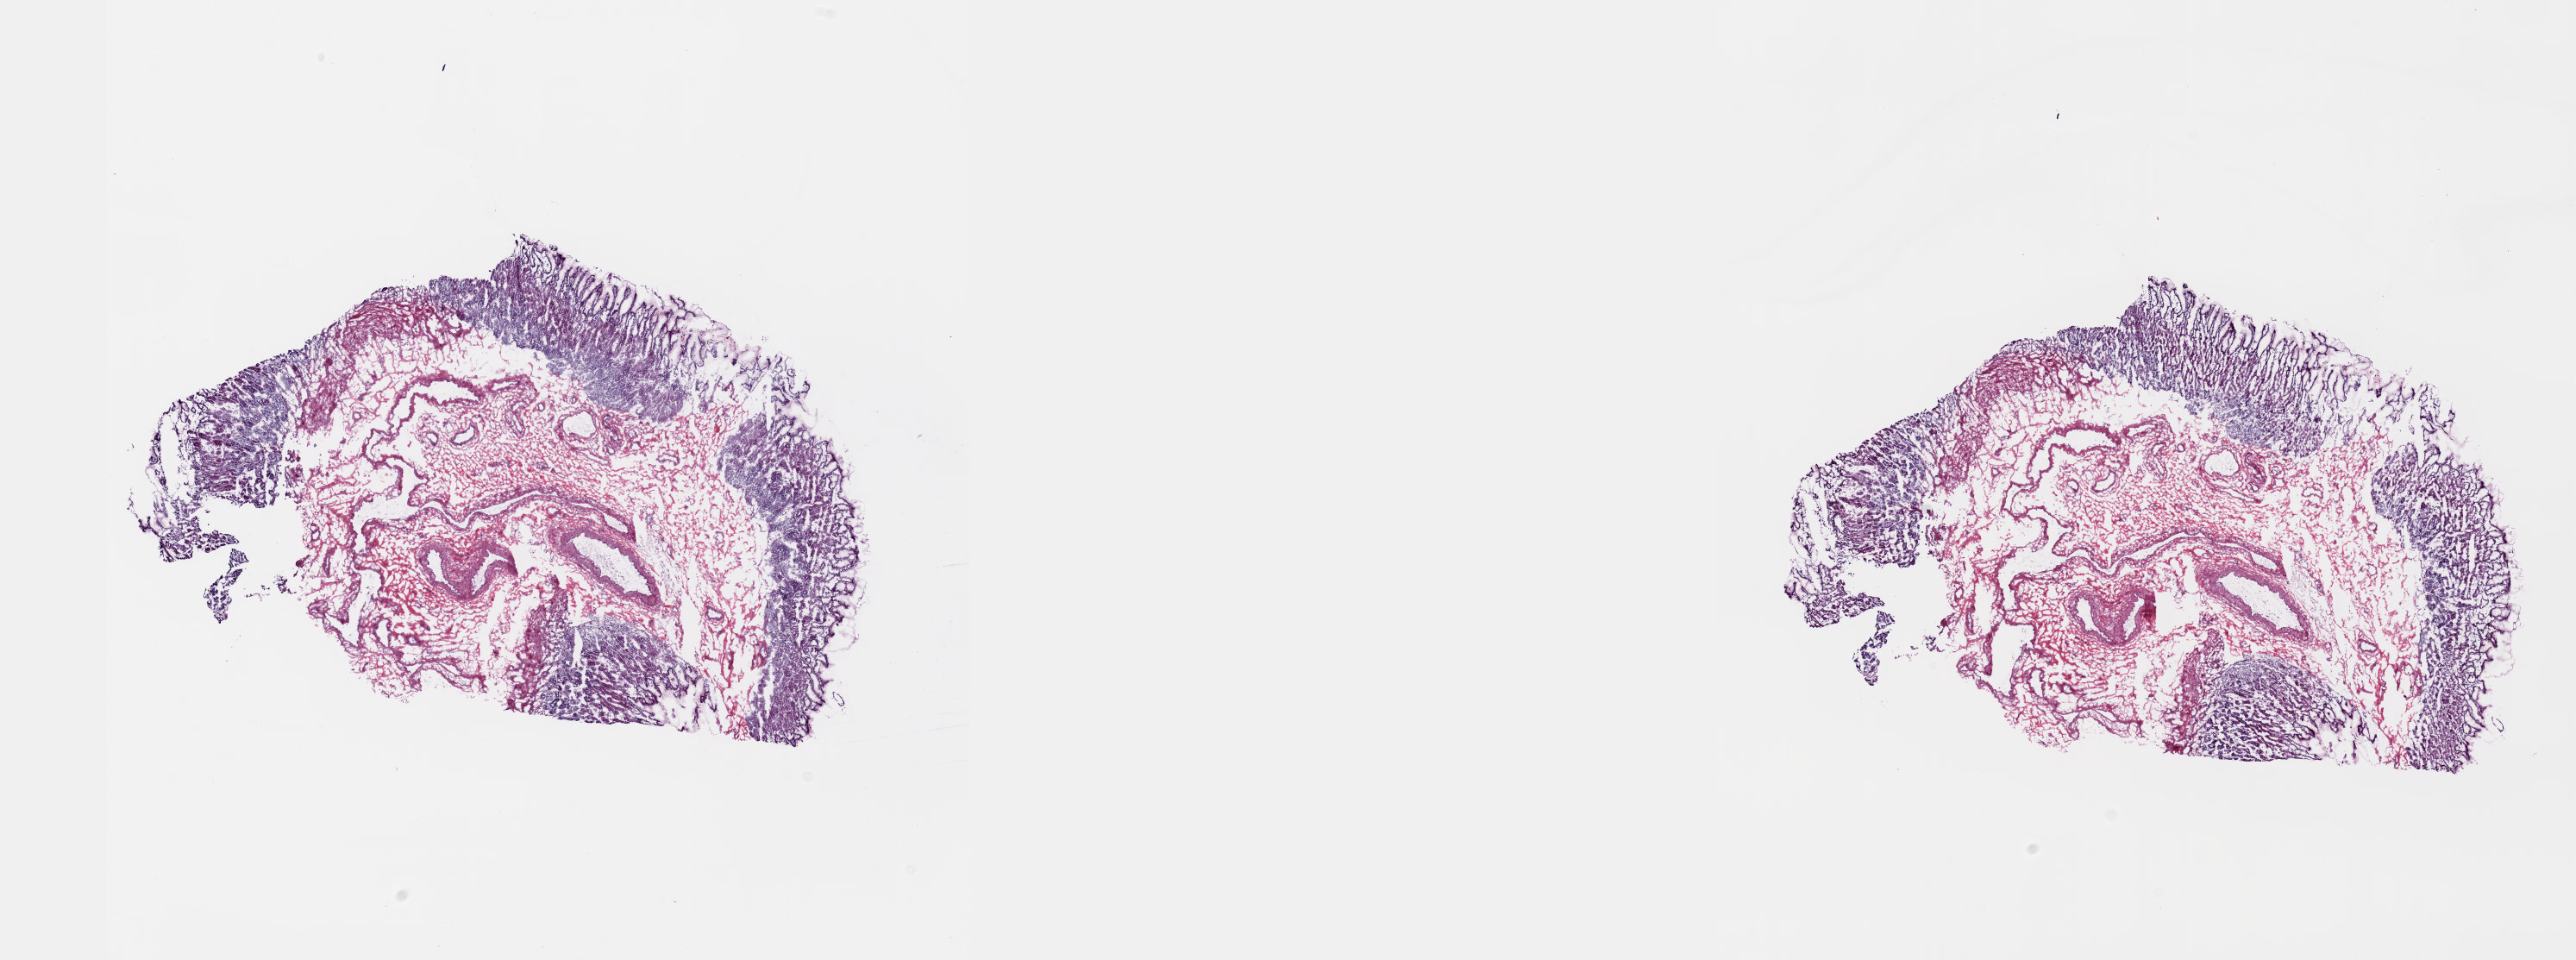
H&E whole-slide image — a low-resolution overview of the entire scanned area, about 24.1 x 9.0 mm, frozen section from the top of the tissue portion, sample: solid tissue normal (non-tumour tissue), esophagus. Male, age 84 years at initial diagnosis.
This section: solid tissue normal sample (biorepository sample class). Patient diagnosis: Squamous cell carcinoma, NOS (lower third of esophagus).